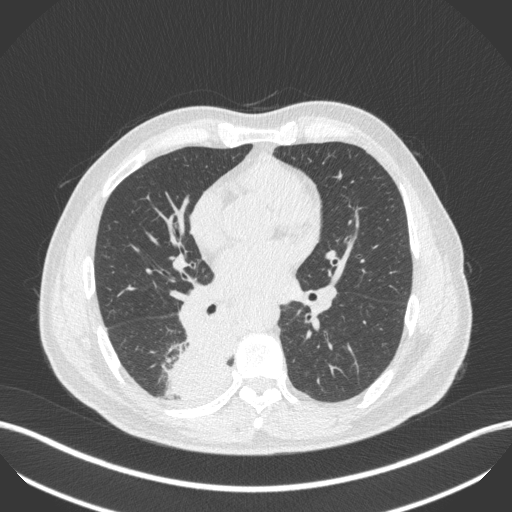
Chest CT, one axial slice; position 234 of 451 along the scan axis; reconstruction kernel B31f; 100 kVp; lung window (W 1500 / L -600 HU); 1 mm slice thickness; 512 × 512 image matrix, field of view 400 × 400 mm. Patient: male, 61 years. Case-level facts recorded for this patient, not image findings: clinical TNM (as recorded): T1 N0 M0; histopathological grade: G3.
Structures marked on this image (bounding box drawn by a radiologist):
- lung tumour (recorded histology: small cell carcinoma): bounding box (x1, y1, x2, y2) in pixels: (163, 316, 233, 404)